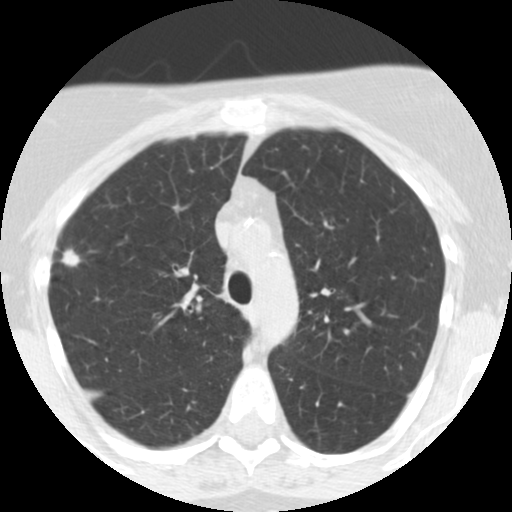
Low-dose screening chest CT, one axial slice; reconstruction kernel STANDARD; lung window (W 1500 / L -600 HU); 512 × 512 image matrix.
Outlined on this slice (expert manual segmentation):
- lesion 1 (tumor, upper lobe of right lung): bounding box (x1, y1, x2, y2) in pixels: (62, 250, 80, 266)